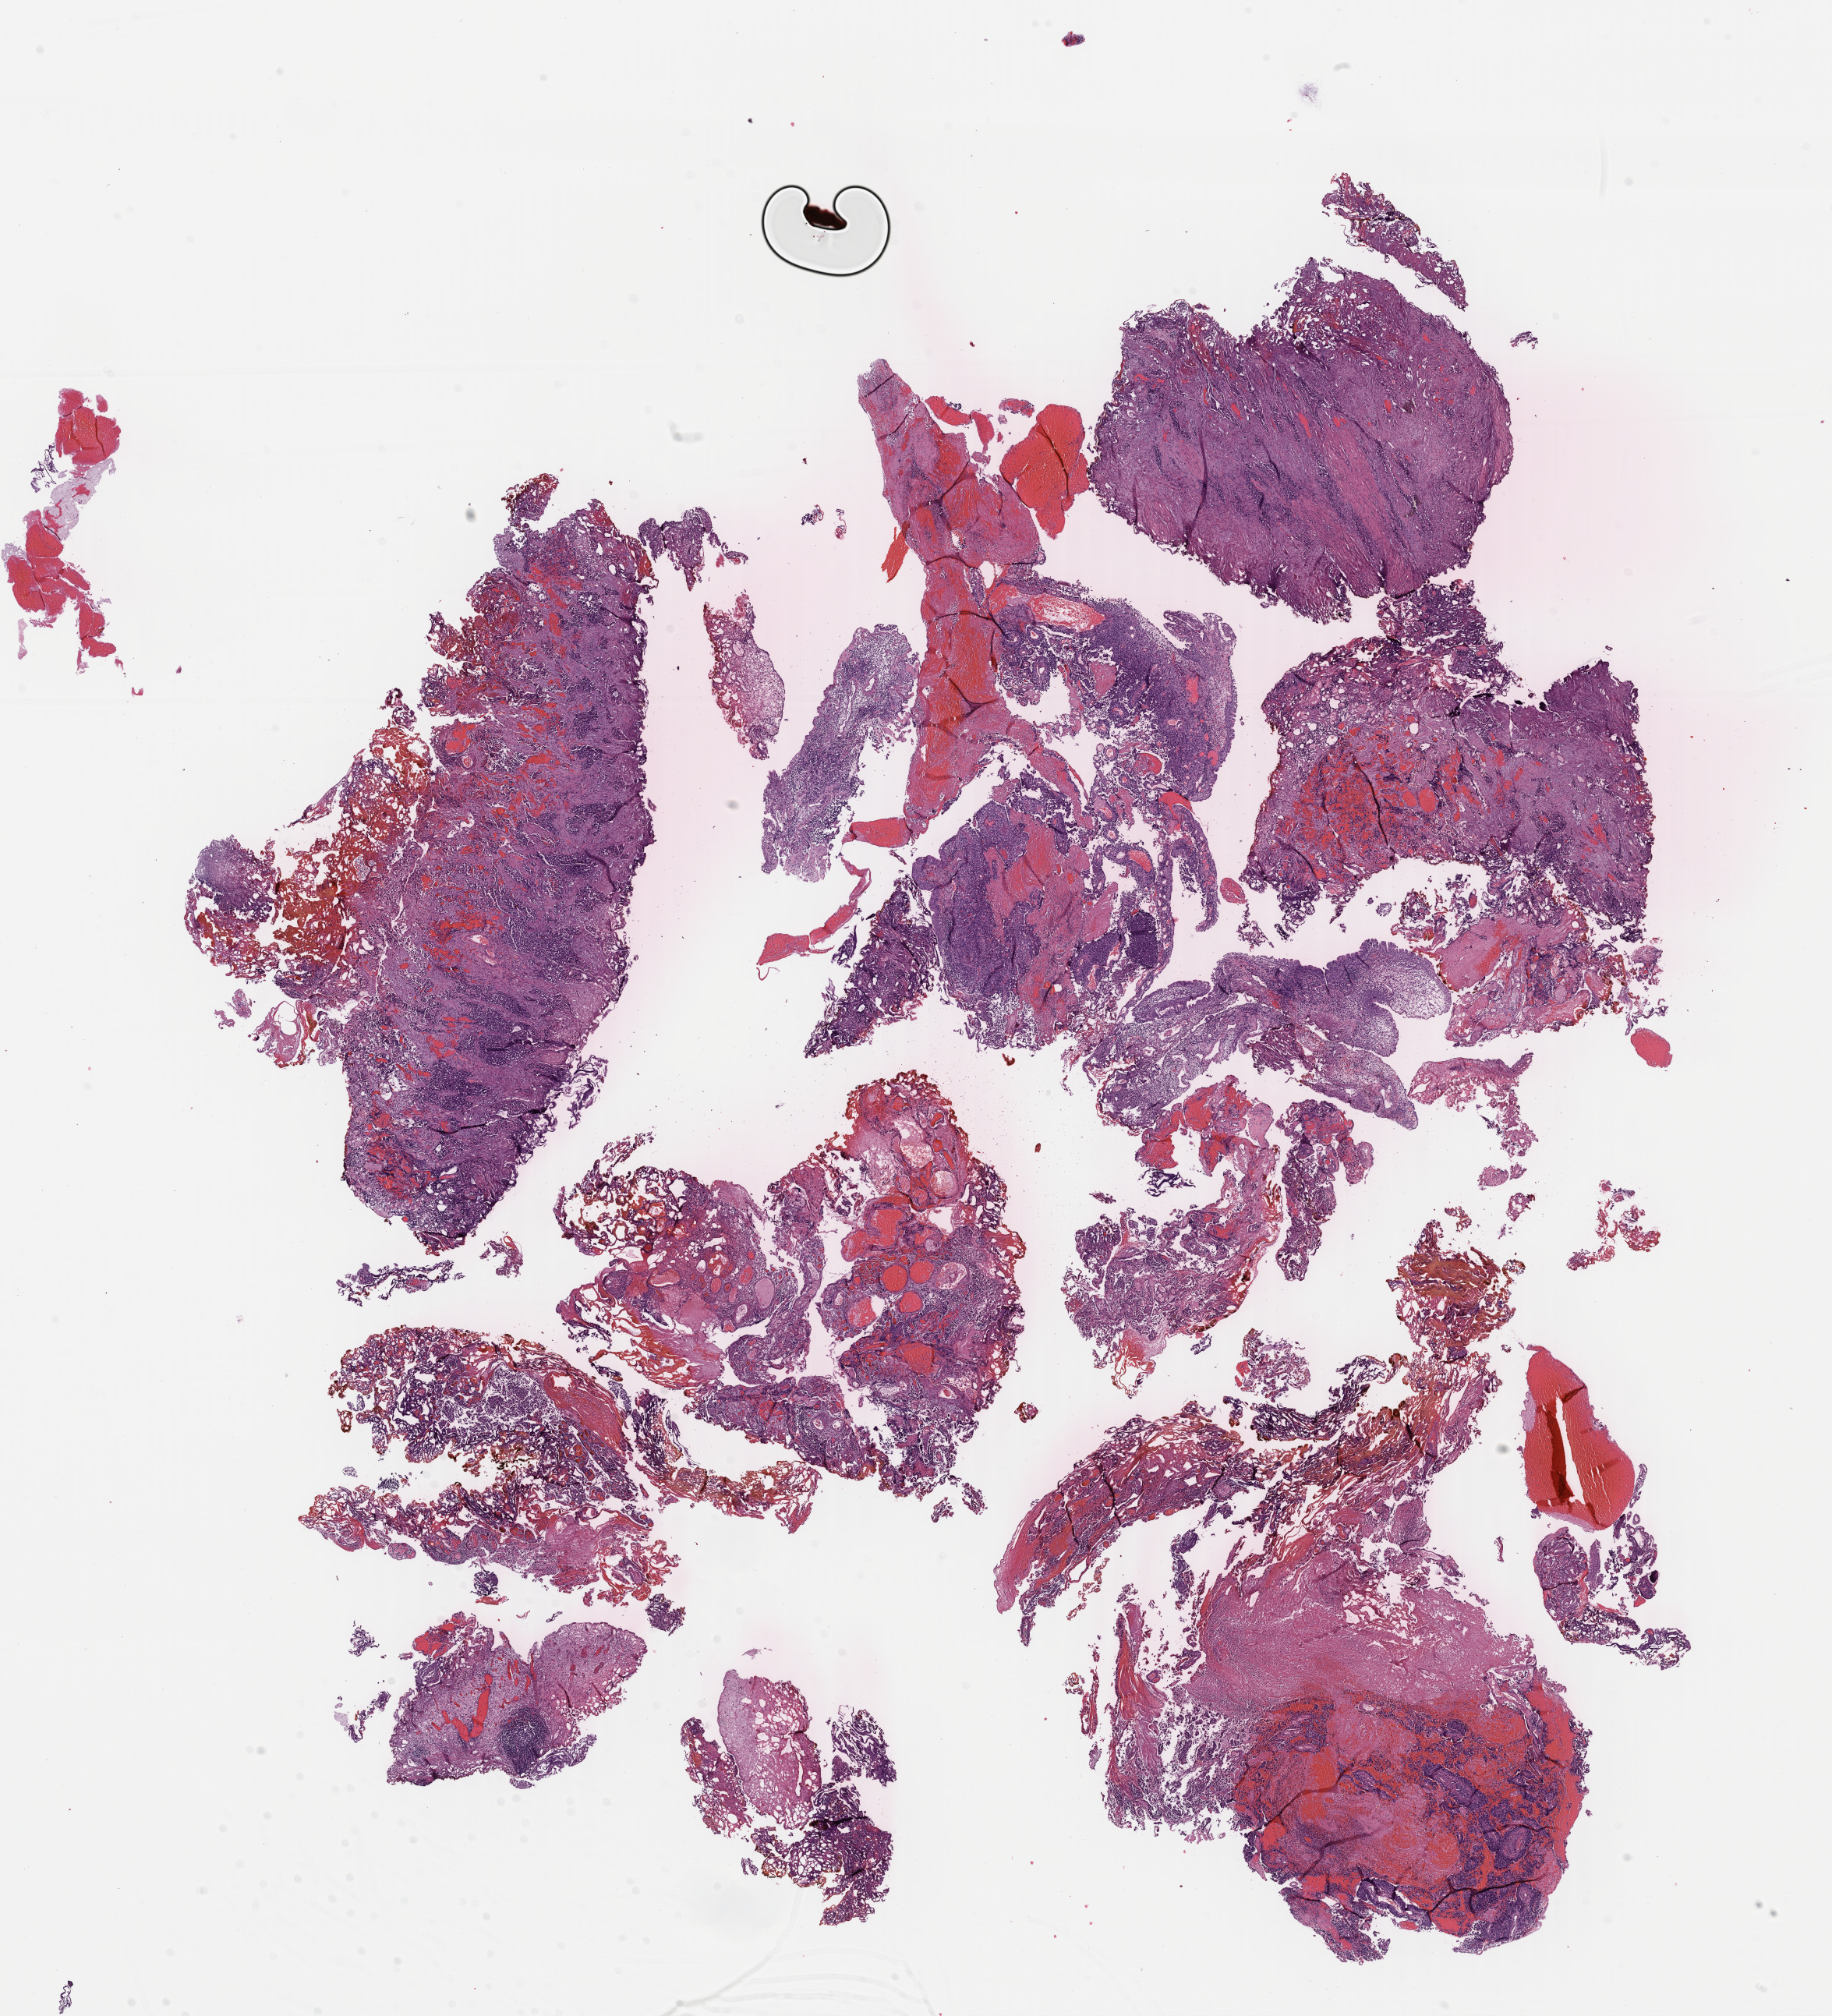
Hematoxylin and eosin (H&E) stained whole-slide image — low-resolution overview of the scanned area, about 18.5 x 20.3 mm (acquisition: 40x scan), formalin-fixed paraffin-embedded (FFPE) diagnostic section, bladder, primary tumour sample. Male, age 73 years at initial diagnosis. Histologic grade: high grade.
* AJCC pathologic stage: III
* TNM: N0 M0
* pathologic diagnosis: Papillary transitional cell carcinoma